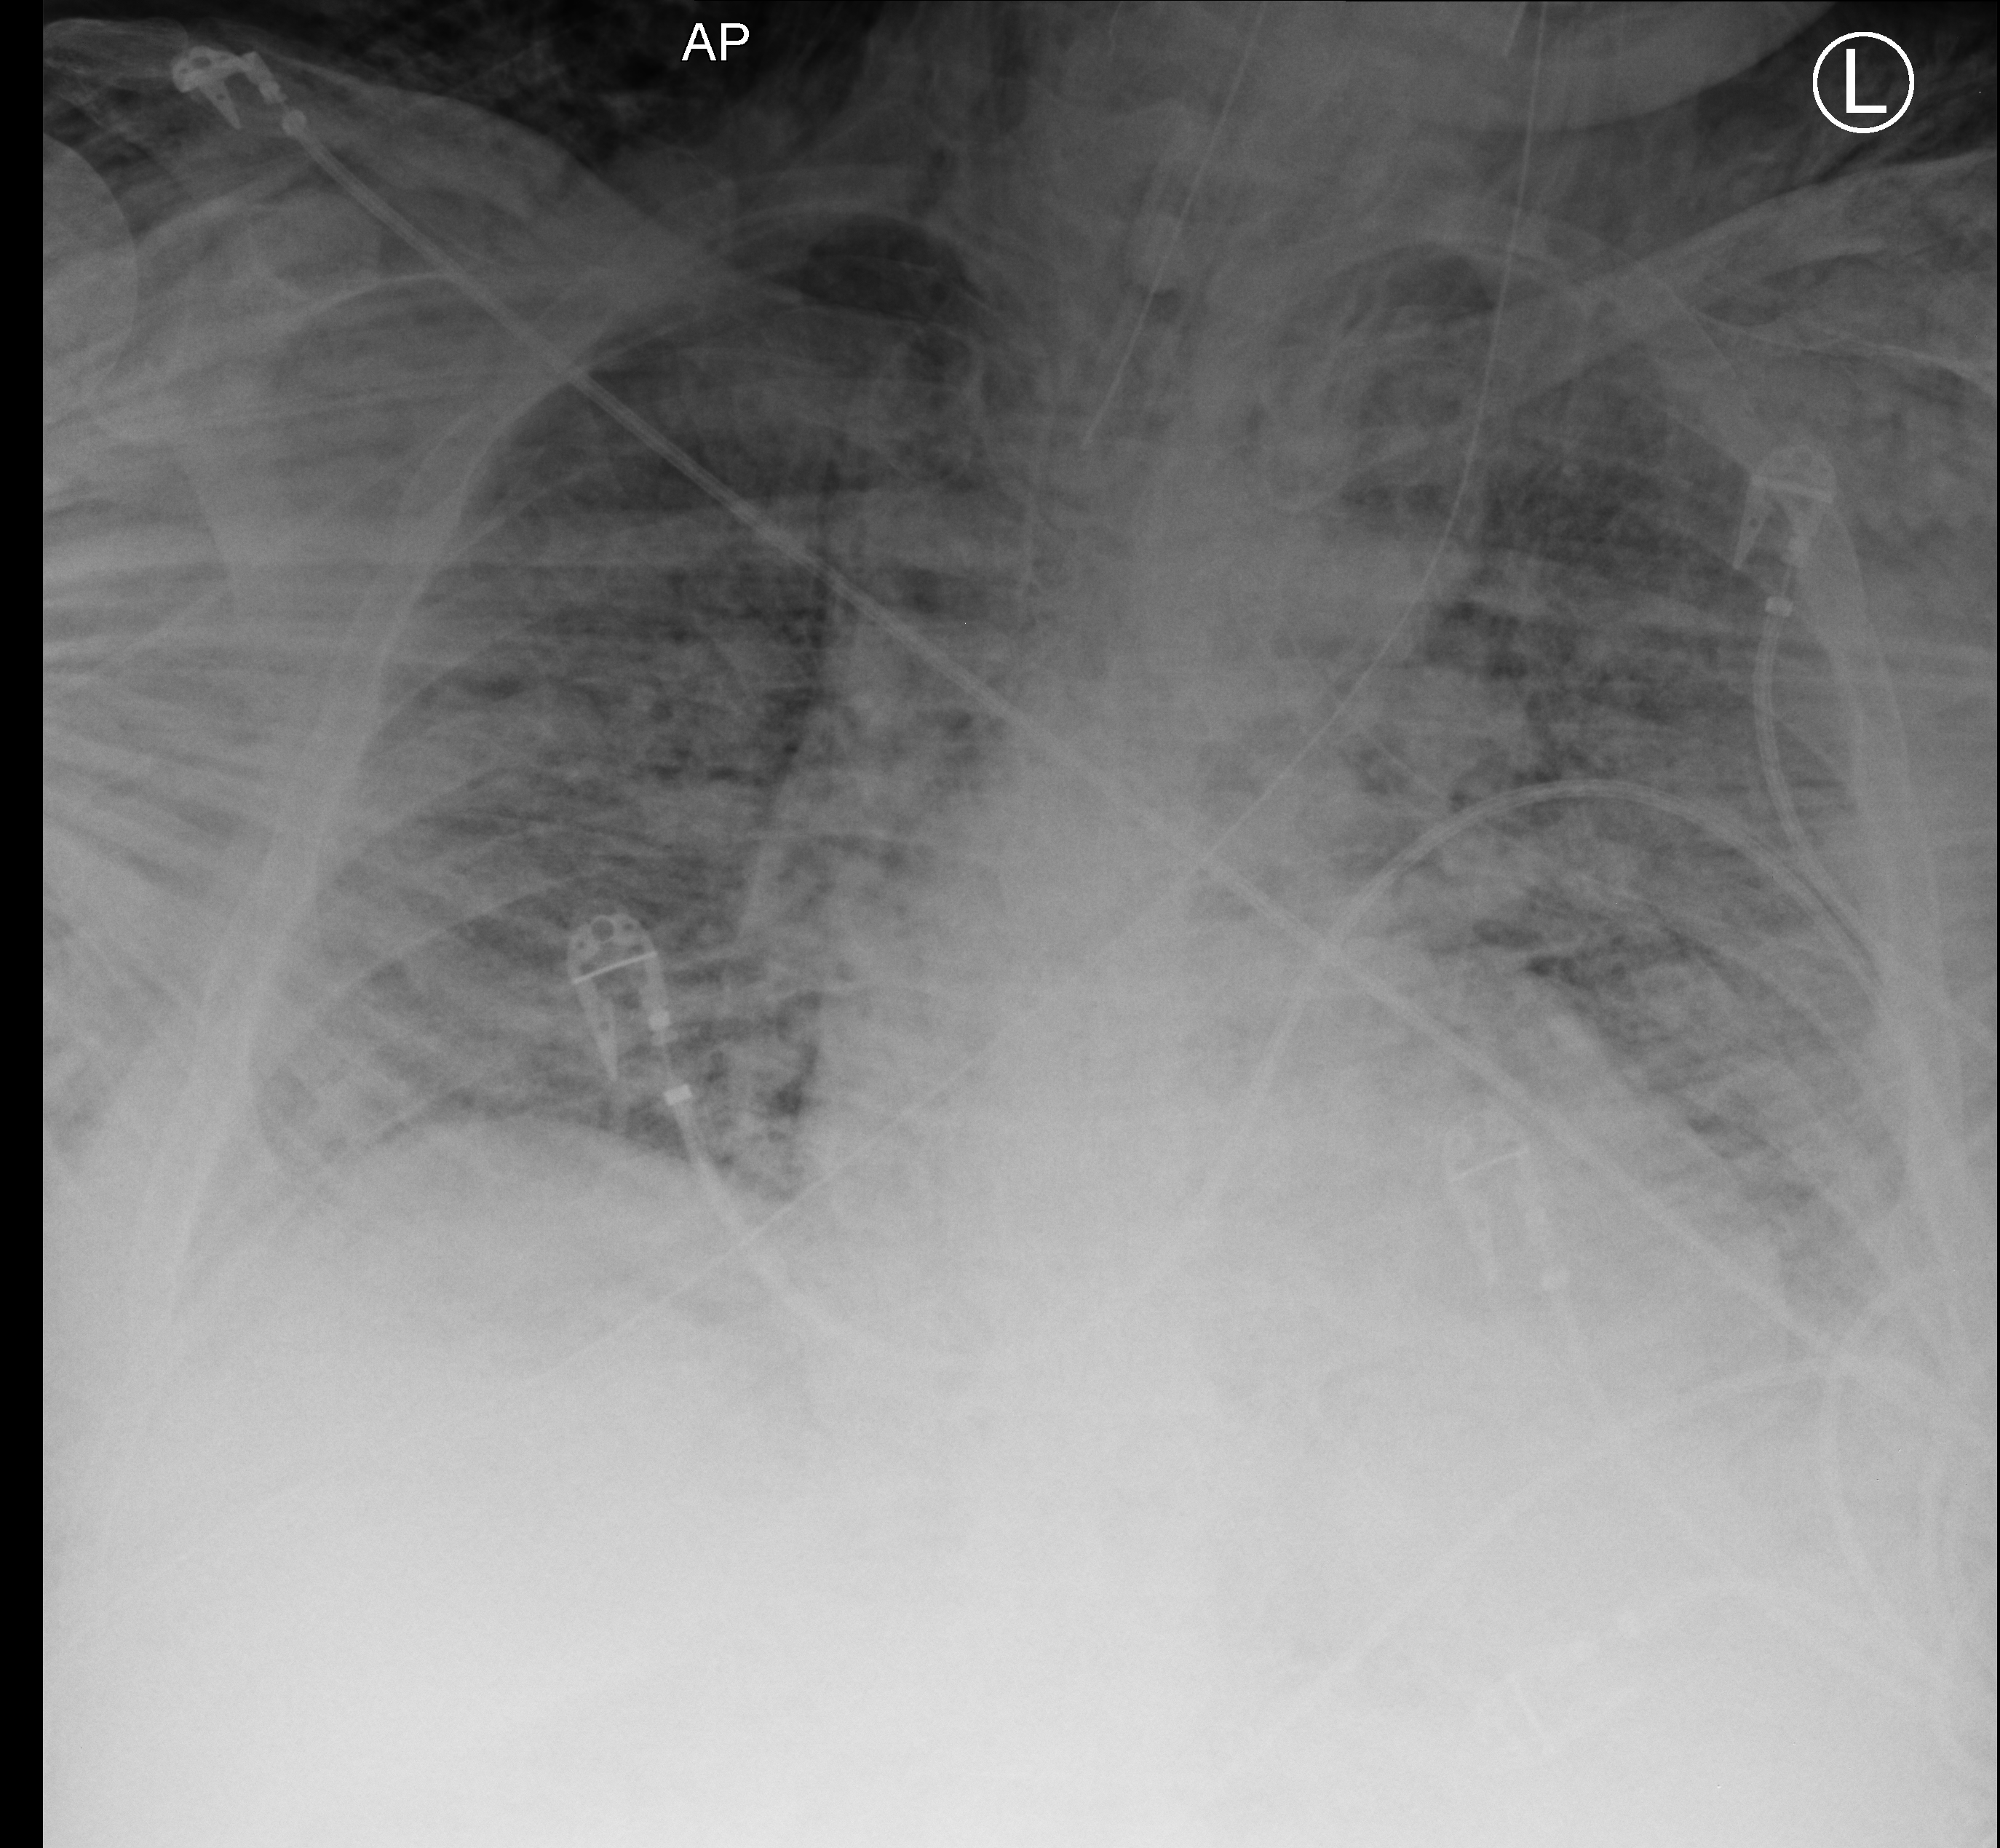
Bedside chest radiograph (computed radiography); anteroposterior (AP) projection. Adult patient hospitalised with COVID-19, age 18–59 years.
From the hospital-stay record, not from the radiograph (when in the stay this image was taken is not recorded): admitted to intensive care during this hospital stay: yes; length of hospital stay: 26 days.